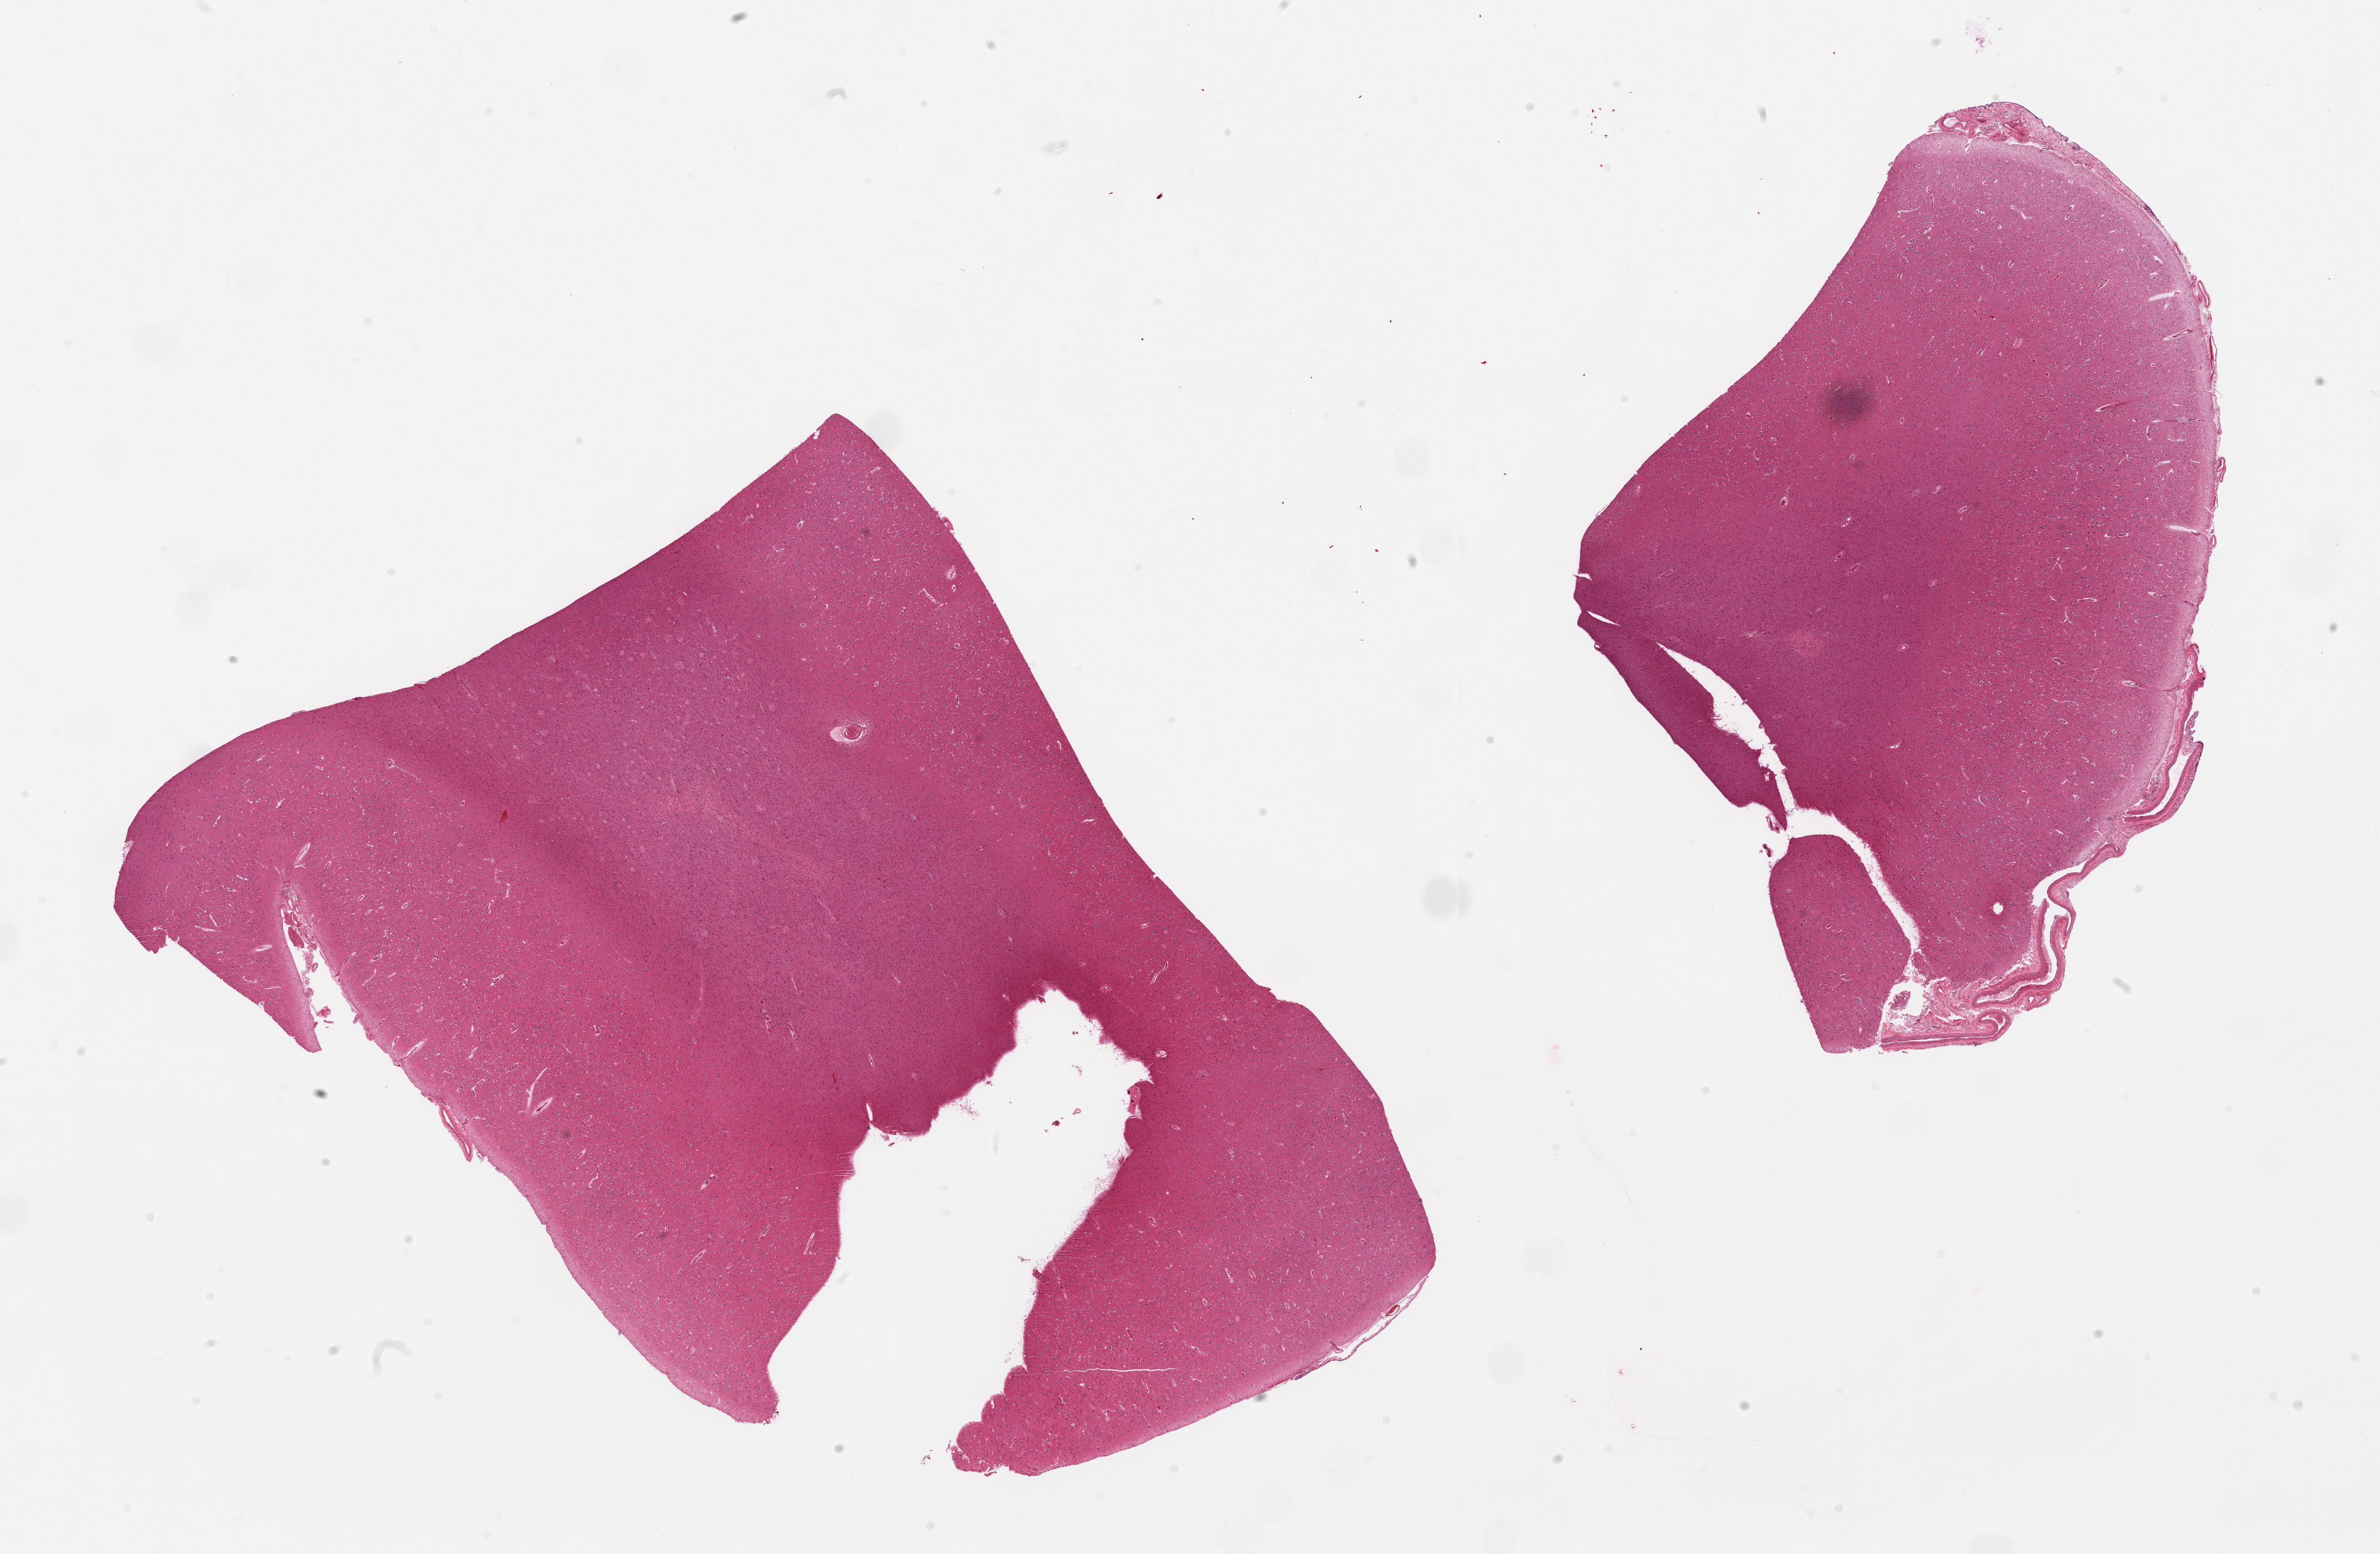
Whole-slide image, haematoxylin and eosin stain — low-resolution overview of the scanned area, about 30.5 x 19.9 mm (slide scanned at 20x). PAXgene-fixed, paraffin-embedded tissue. Target tissue: cerebral cortex. Tissue donor sample. Donor sex: female.
Pathologist's review note for this sample: 2 pieces; meningeal vessels on edge of 1 piece.